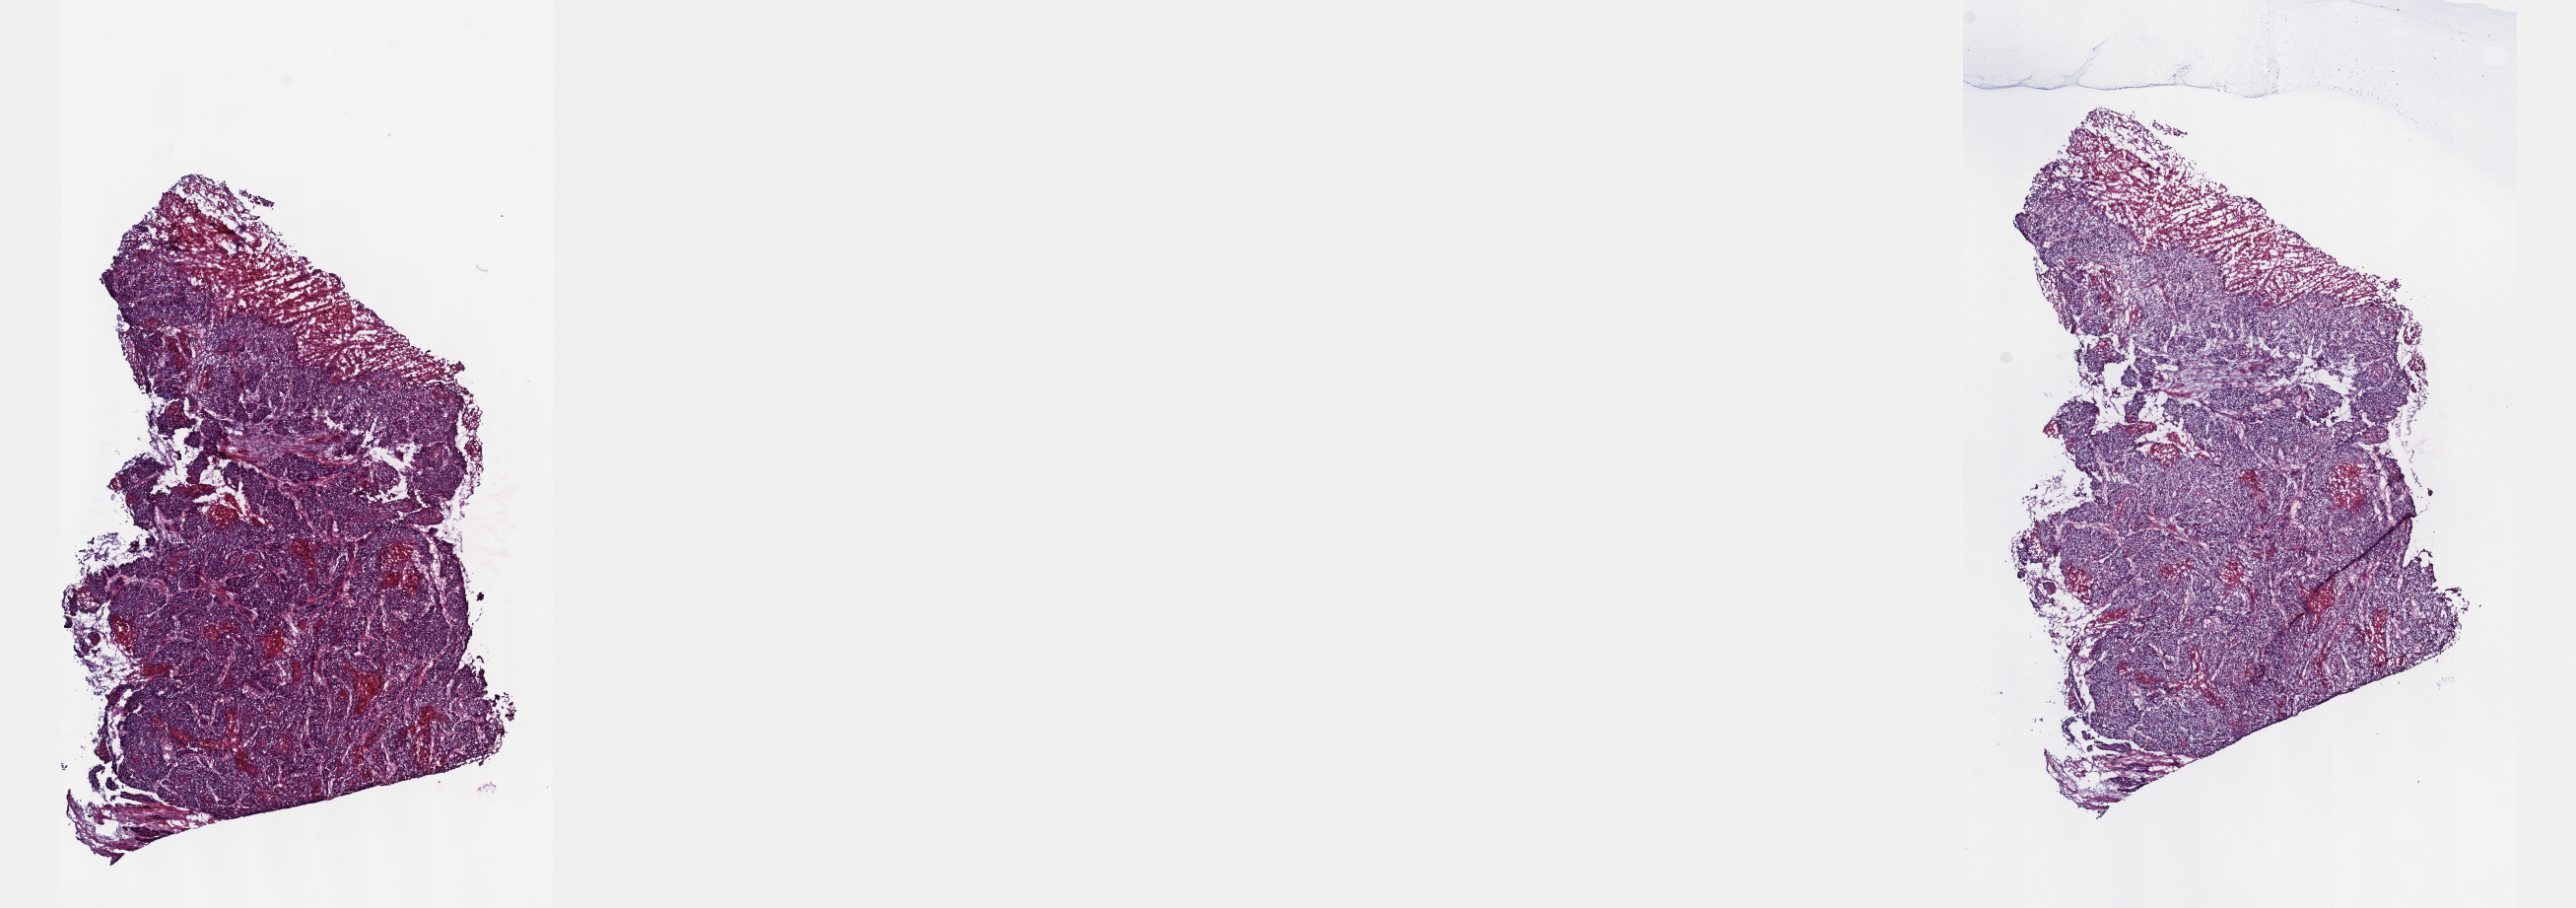
Digitized H&E tissue section (whole slide) — shown as a low-resolution overview of the whole scanned area (about 21.1 x 7.4 mm, acquisition: 40x scan); frozen section from the top of the tissue portion; sample: primary tumour, cervix. Female patient; age at initial diagnosis 25 years. Pathologist review of this section (percent, as recorded): tumour cells 80%, tumour nuclei 95%, normal cells 0%, stromal cells 20%, necrosis 0%. Infiltration values recorded for this section: lymphocyte infiltration 0%, monocyte infiltration 0%, neutrophil infiltration 0%.
Histologic diagnosis: Squamous cell carcinoma, keratinizing, NOS (cervix uteri). FIGO stage: IIB.